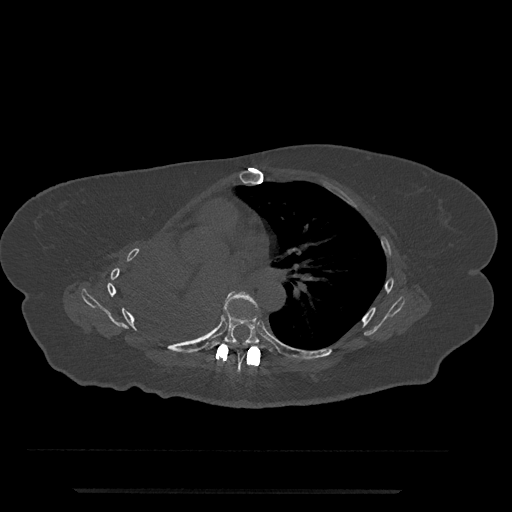
CT including the spine, one axial slice; reconstruction kernel Br40s/3; 120 kVp; bone window (W 1800 / L 400 HU); 0.5 mm slice thickness; 512 × 512 image matrix, field of view 440 × 440 mm. Patient: female, 51 years. Case-level facts recorded for this patient, not image findings: primary cancer: neuro; vertebrae with lytic lesions (as recorded): T8.
Outlined on this slice (semi-automatic segmentation, software-assisted and operator-edited):
- T6 vertebra: bounding box [x1, y1, x2, y2] px = [225, 309, 246, 372]
- T7 vertebra: [205, 294, 277, 355]